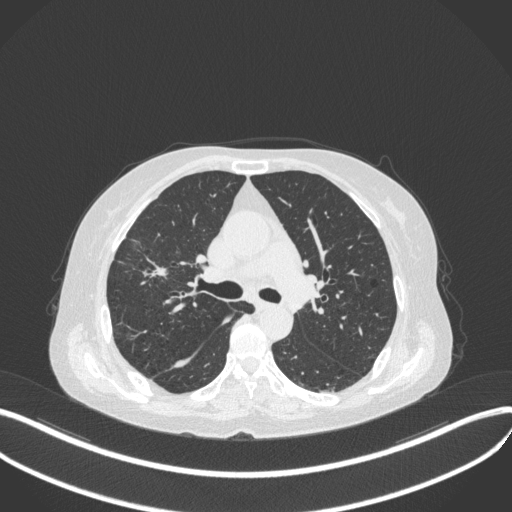
Chest CT, one axial slice; position 255 of 429 along the scan axis; reconstruction kernel B31f; 120 kVp; lung window (W 1500 / L -600 HU); 512 × 512 image matrix. Female patient, age 69 years. From the clinical record (not read from this slice): clinical TNM (as recorded): T1b N3 M0.
Annotated regions visible in this slice (bounding box drawn by a radiologist):
- lung tumour (recorded histology: small cell carcinoma): box from (x=137, y=252) to (x=174, y=283) px